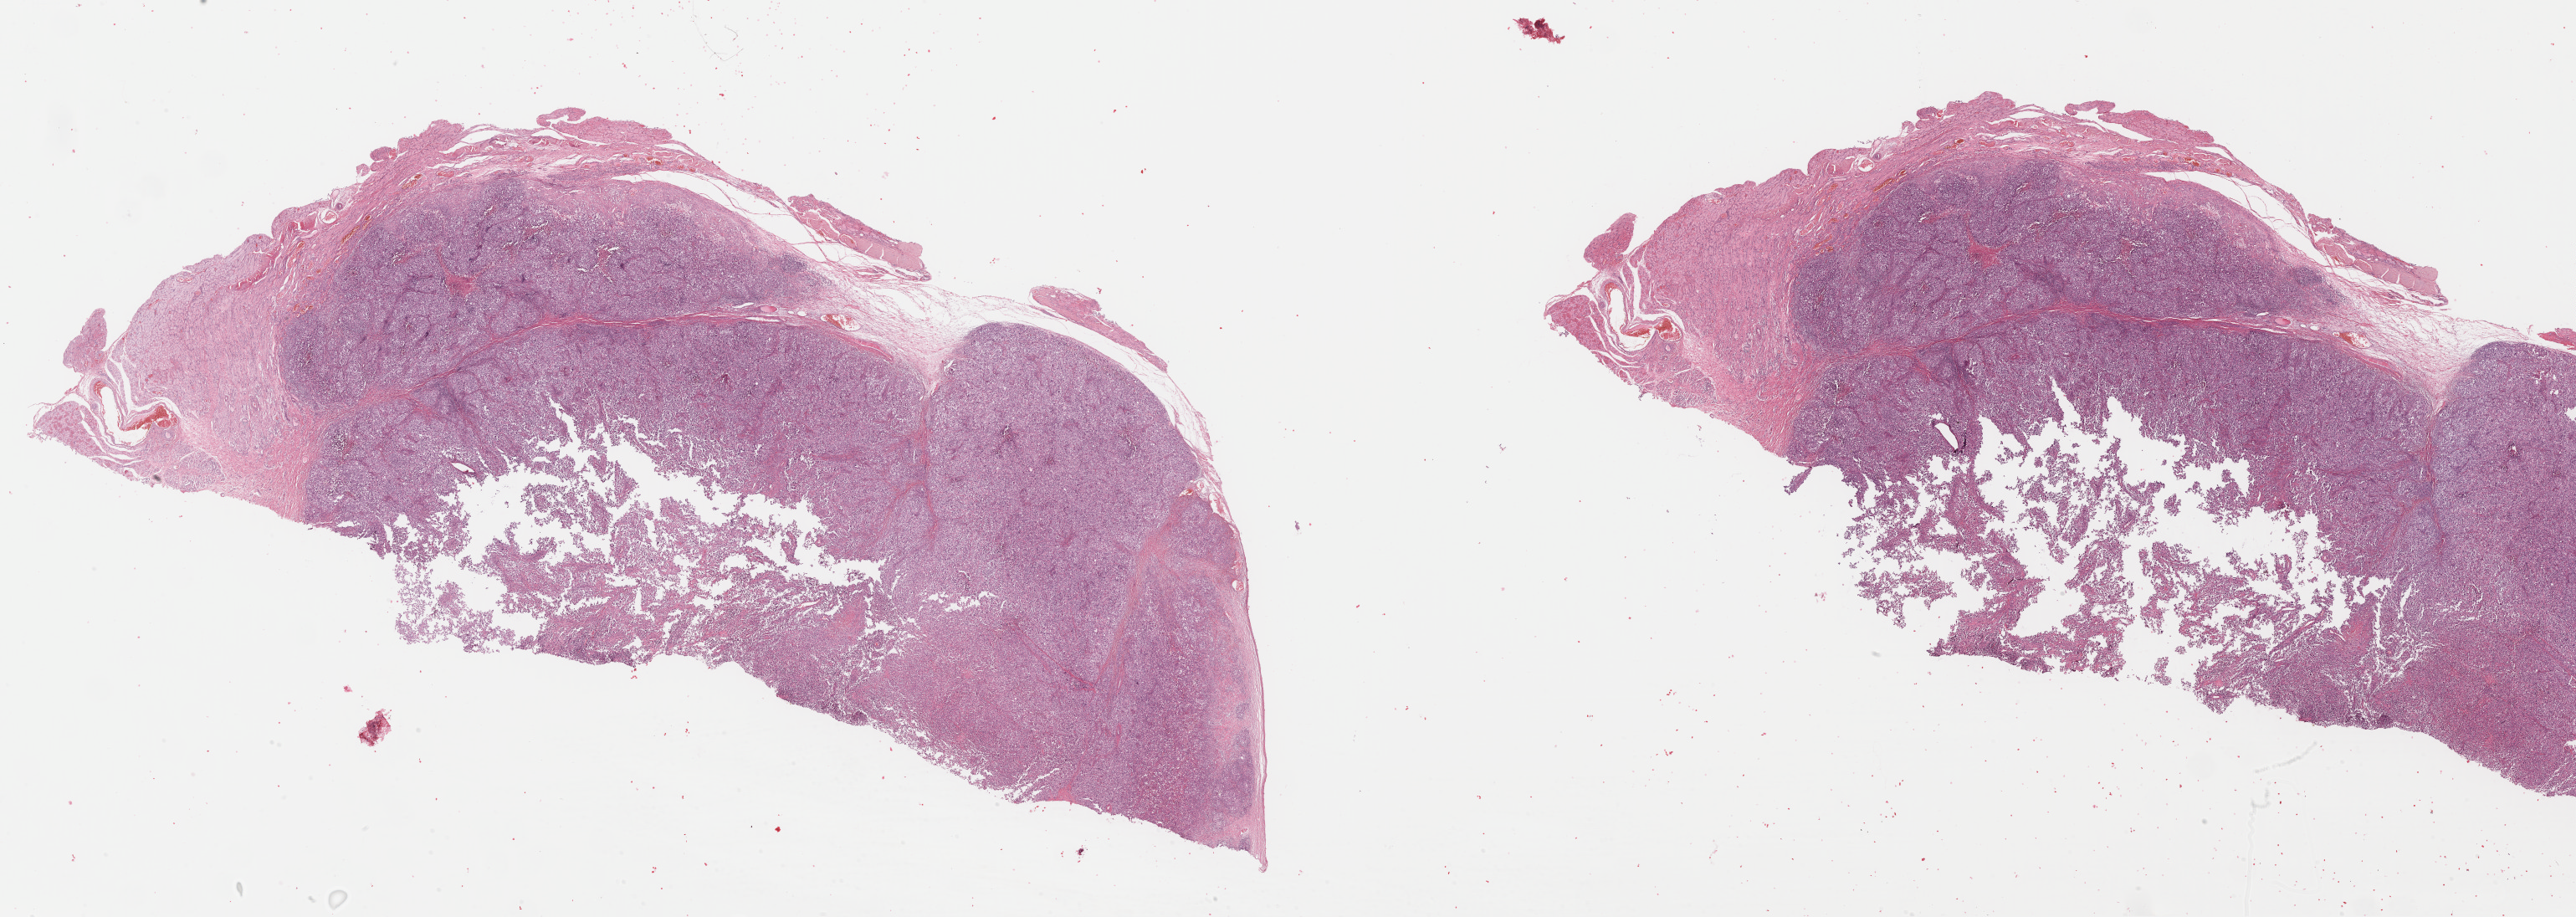
Digitized H&E tissue section (whole slide), low-resolution overview of the scanned area, about 48.4 x 17.2 mm (slide scanned at 40x); formalin-fixed paraffin-embedded (FFPE) diagnostic section; metastatic tumour sample, sampled site: lymph node. Patient: male, age at initial diagnosis 74 years.
- this section: metastatic tumour tissue
- patient diagnosis: Malignant melanoma, NOS